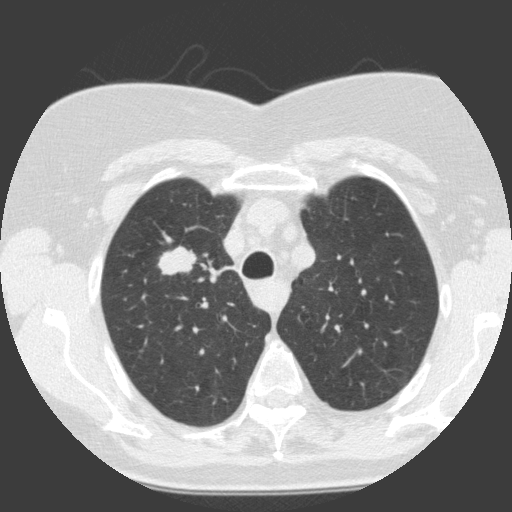
Chest CT (low-dose screening protocol), one axial image. Baseline screening round. Lung window (W 1500 / L -600 HU). Female, age 68 years at enrolment. Current smoker at enrolment.
Lesion marked by an expert reader, box from (x=155, y=239) to (x=203, y=284) px. The exam's reader record, not a measurement of the box and not confirmed to be the same lesion: non-calcified nodule or mass ≥4 mm, right upper lobe, 19 × 12 mm, smooth margins, soft tissue attenuation. Participant outcome: lung cancer diagnosed 30 days after this screen — squamous cell carcinoma, NOS, right upper lobe, moderately differentiated (G2), stage IA (AJCC 6th edition), 28 mm at pathology.